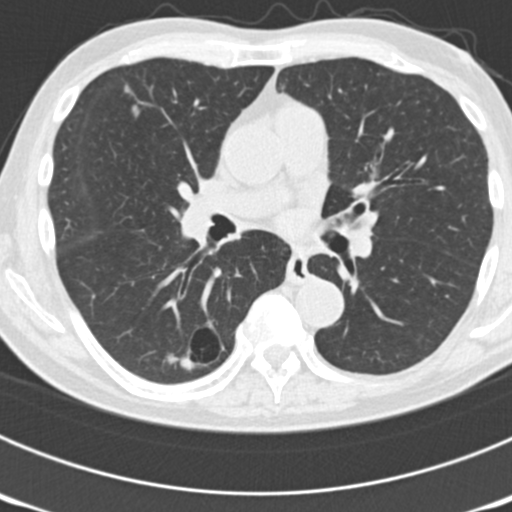
Low-dose screening chest CT, one axial slice; position 102 of 177 along the scan axis; lung window (W 1500 / L -600 HU); 2 mm slice thickness; 512 × 512 image matrix, field of view 300 × 300 mm.
Annotated regions visible in this slice (expert manual segmentation):
- lesion 5 (nodule, lower lobe of right lung): box from (x=177, y=355) to (x=194, y=372) px